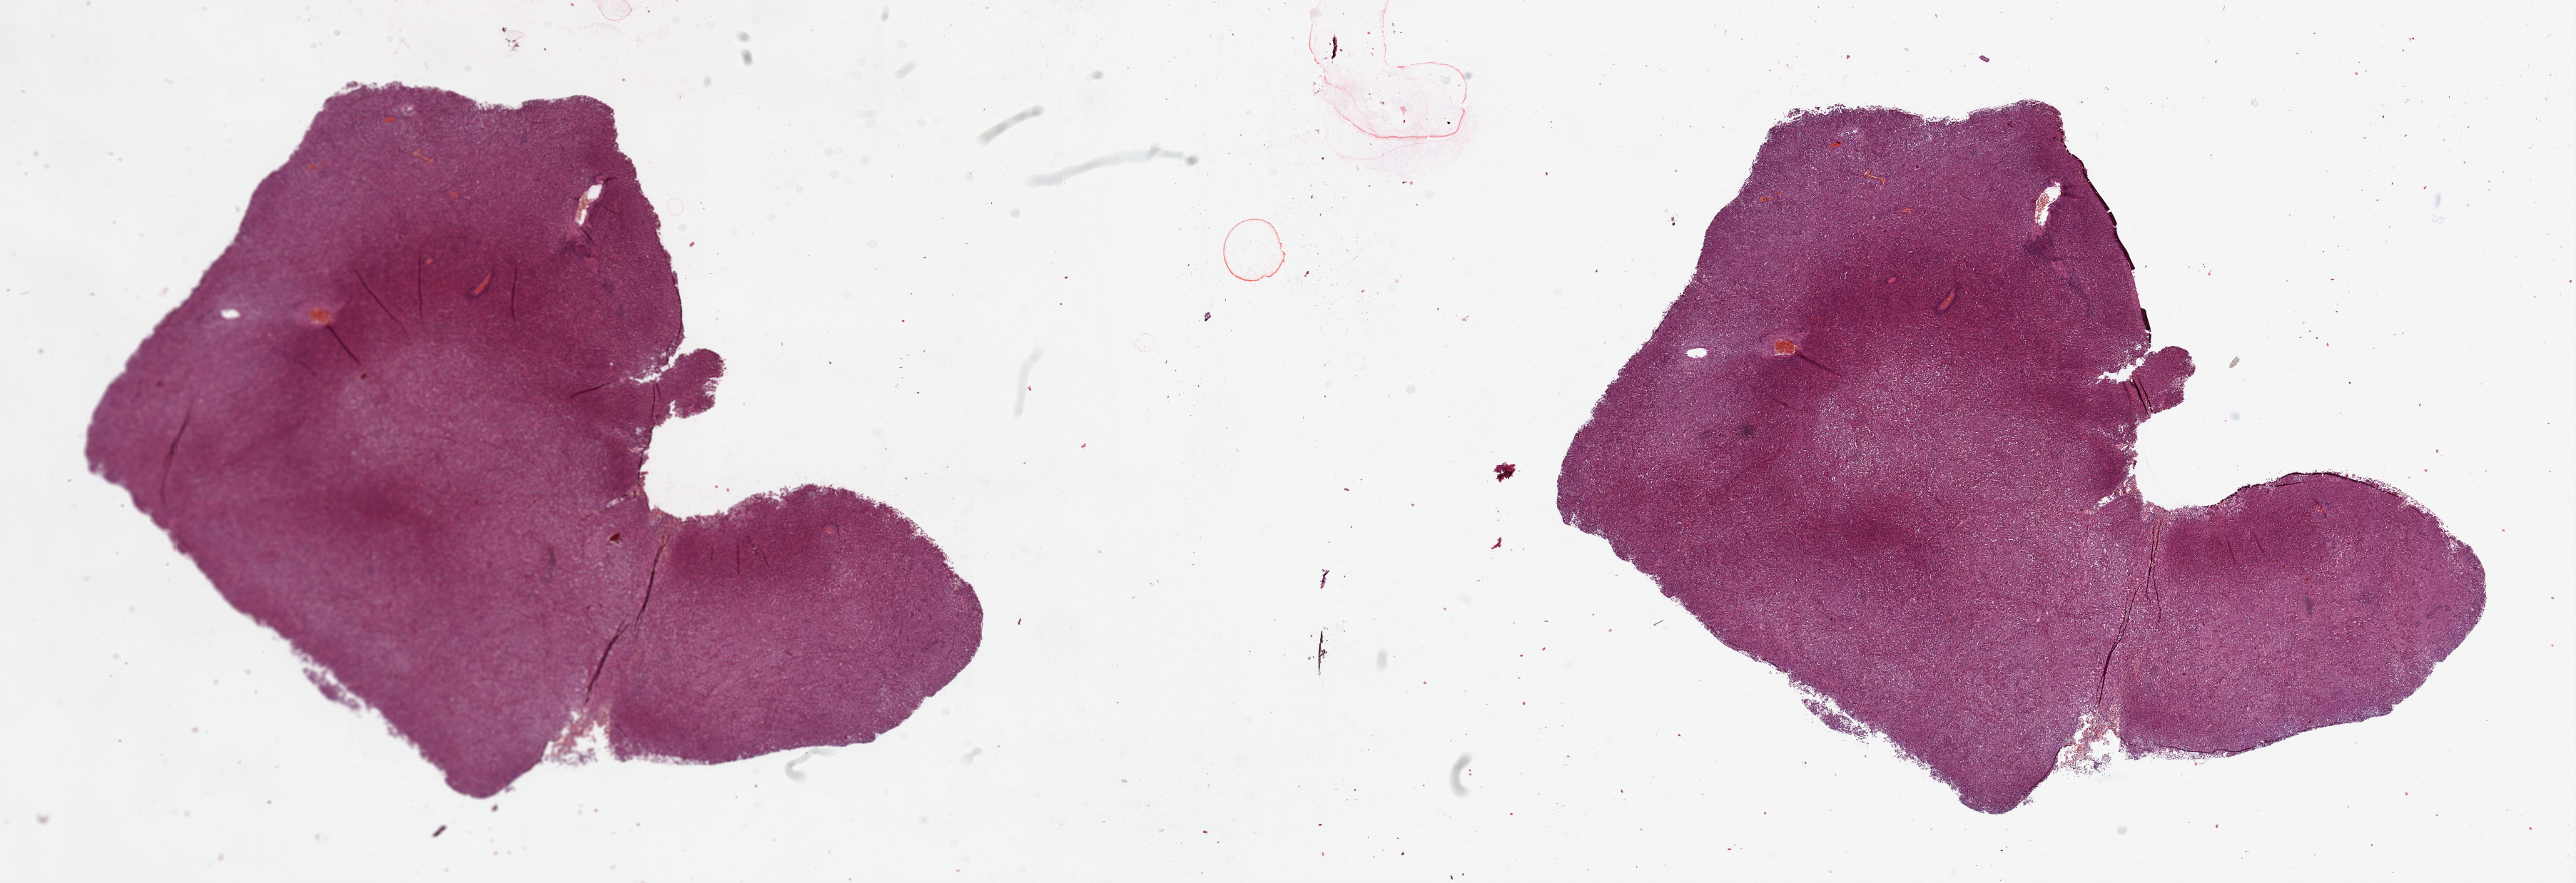
H&E-stained whole-slide image, low-resolution overview of the scanned area, about 28.5 x 9.8 mm; tumour tissue sample, lung. Patient: male, age 56 years. Histologic grade: G3 (poorly differentiated).
Histologic diagnosis: Adenocarcinoma, NOS. AJCC pathologic stage: IIA.